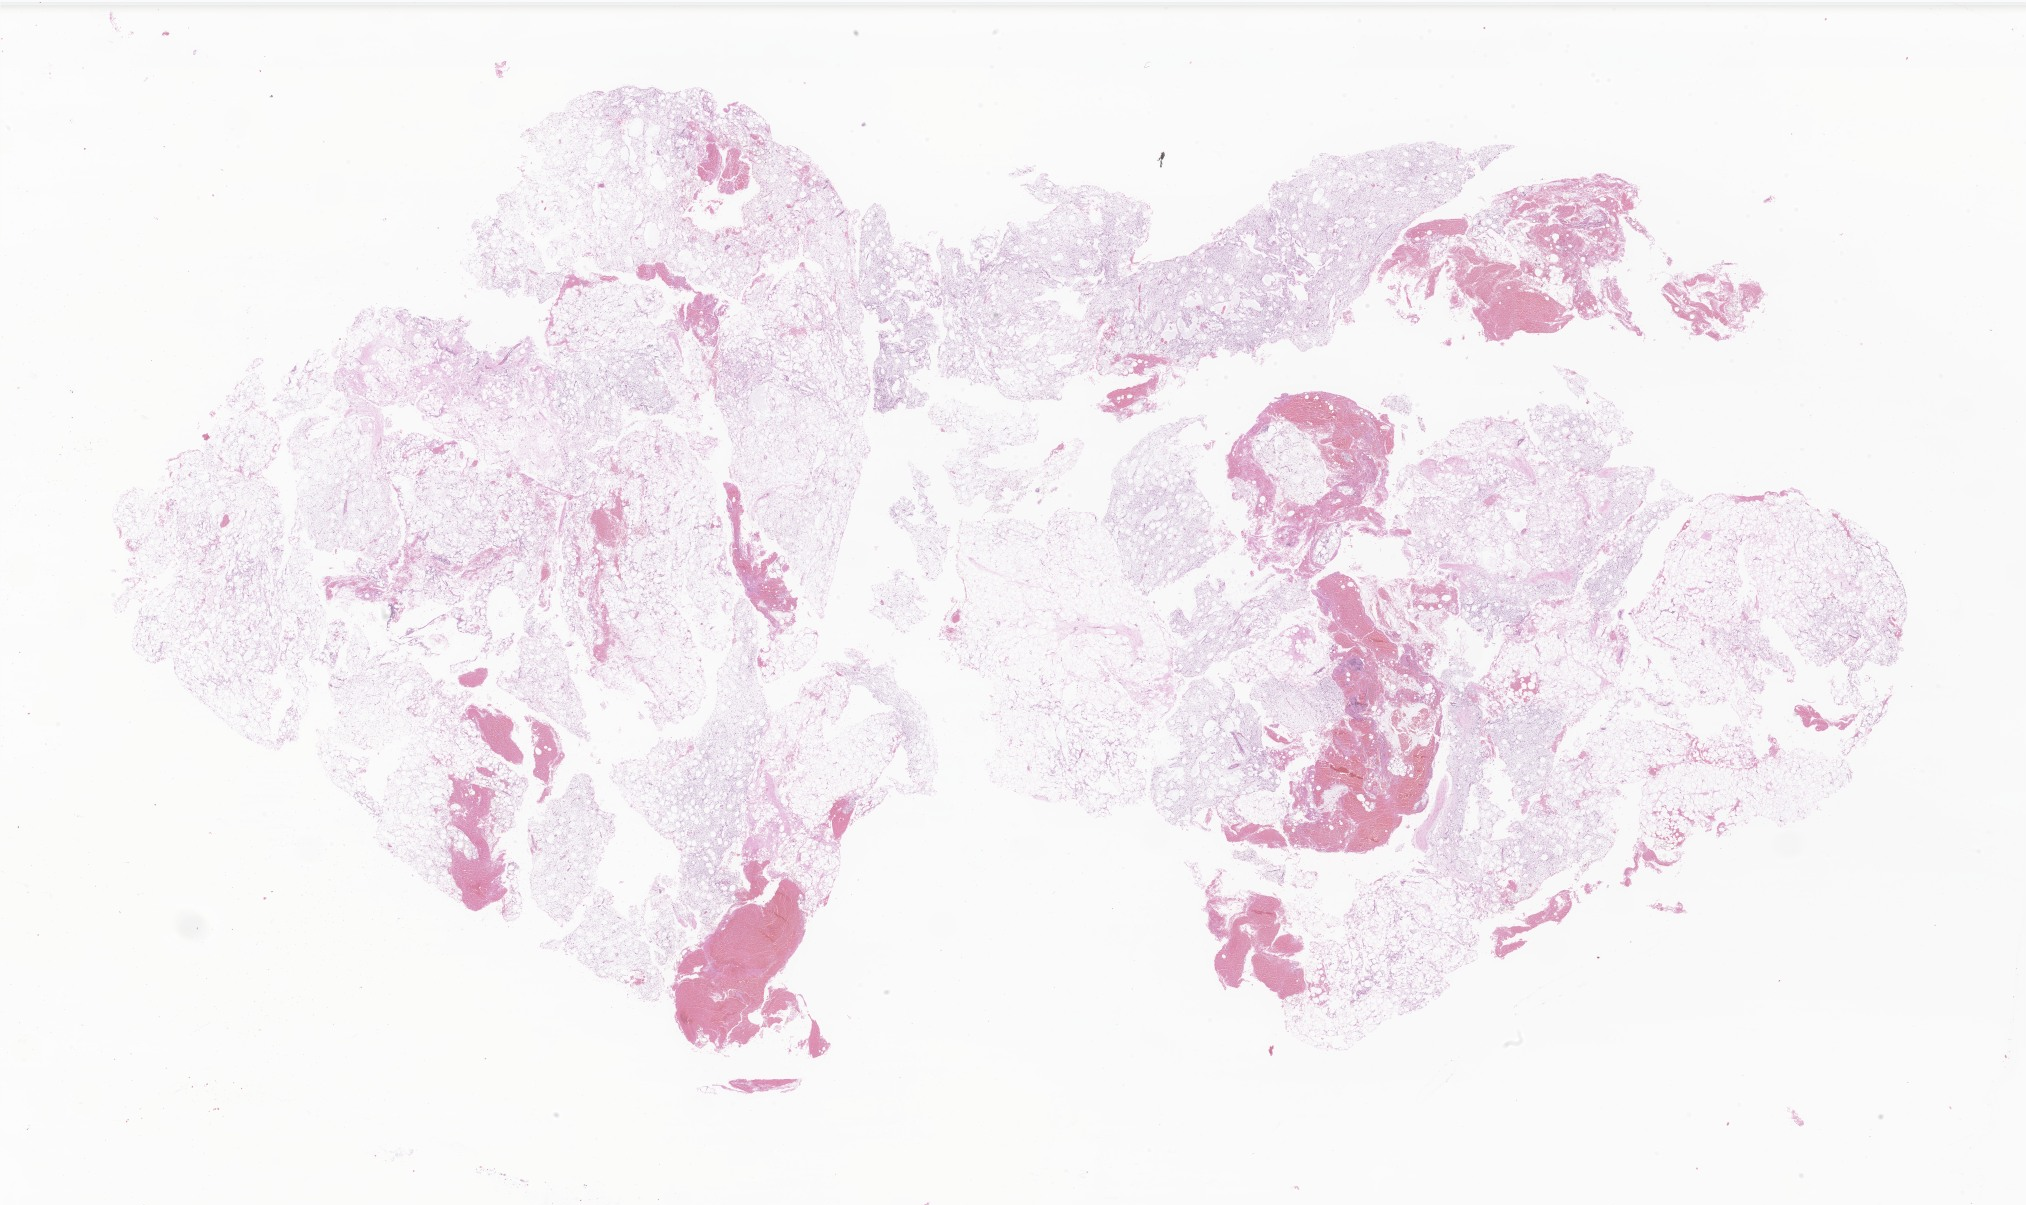
Haematoxylin and eosin whole-slide image of tumor tissue from the soft tissue of lower extremity, whole scanned area (about 34.2 x 20.3 mm) shown as a low-resolution overview. Formalin-fixed, paraffin-embedded (FFPE) tissue. Patient: male, age 209 months (17 years 5 months).
- recorded diagnosis: Myxoid liposarcoma